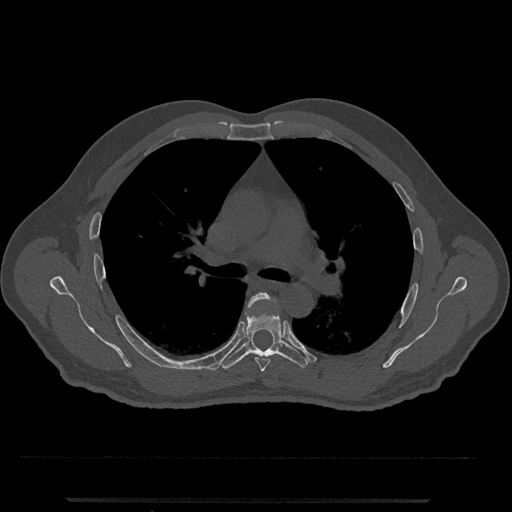
CT including the spine, one axial slice. Position 760 of 797 along the scan axis. 120 kVp. Bone window (W 1800 / L 400 HU). 512 × 512 image matrix, field of view 419 × 419 mm. Male patient, age 63 years. Case-level facts recorded for this patient, not image findings: primary cancer: prostate.
Structures marked on this image (semi-automatic segmentation, software-assisted and operator-edited):
- T5 vertebra: bounding box (x1, y1, x2, y2) in pixels: (245, 293, 276, 372)
- T6 vertebra: (220, 296, 310, 369)